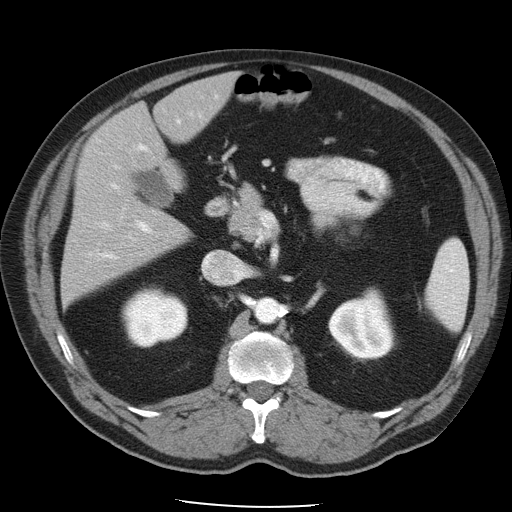
Contrast-enhanced abdominal CT, one axial slice. Reconstruction kernel STANDARD. 120 kVp. Intravenous contrast given. Soft-tissue window (W 400 / L 40 HU). 5 mm slice thickness. 512 × 512 image matrix, field of view 395 × 395 mm. Male patient, age 68 years. Case-level facts recorded for this patient, not image findings: diagnosis: colorectal cancer liver metastases, imaged before liver resection; multiple liver metastases: yes; largest metastasis: 1.7 cm.
Annotated regions visible in this slice (outlined manually by an expert reader):
- hepatic veins: bounding box (x1, y1, x2, y2) in pixels: (100, 165, 248, 283)
- liver: (62, 75, 236, 301)
- planned liver remnant (the part of the liver to remain after resection): (67, 75, 236, 300)
- portal vein (with intrahepatic branches): (89, 95, 219, 260)